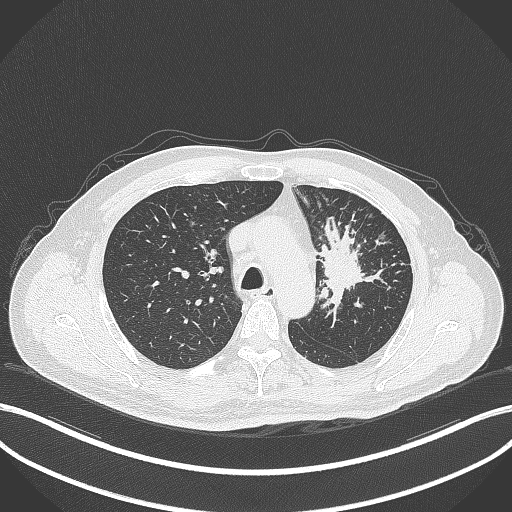
Chest CT, one axial slice. Slice 252 of 386 in the series (ordered by position). Reconstruction kernel B70f. Lung window (W 1500 / L -600 HU). 1 mm slice thickness. 512 × 512 image matrix, field of view 400 × 400 mm. Patient: male, 69 years. Case-level facts recorded for this patient, not image findings: clinical TNM (as recorded): T2a N2 M0.
Structures marked on this image (bounding box drawn by a radiologist):
- lung tumour (recorded histology: adenocarcinoma): bounding box (x1, y1, x2, y2) in pixels: (315, 214, 373, 312)